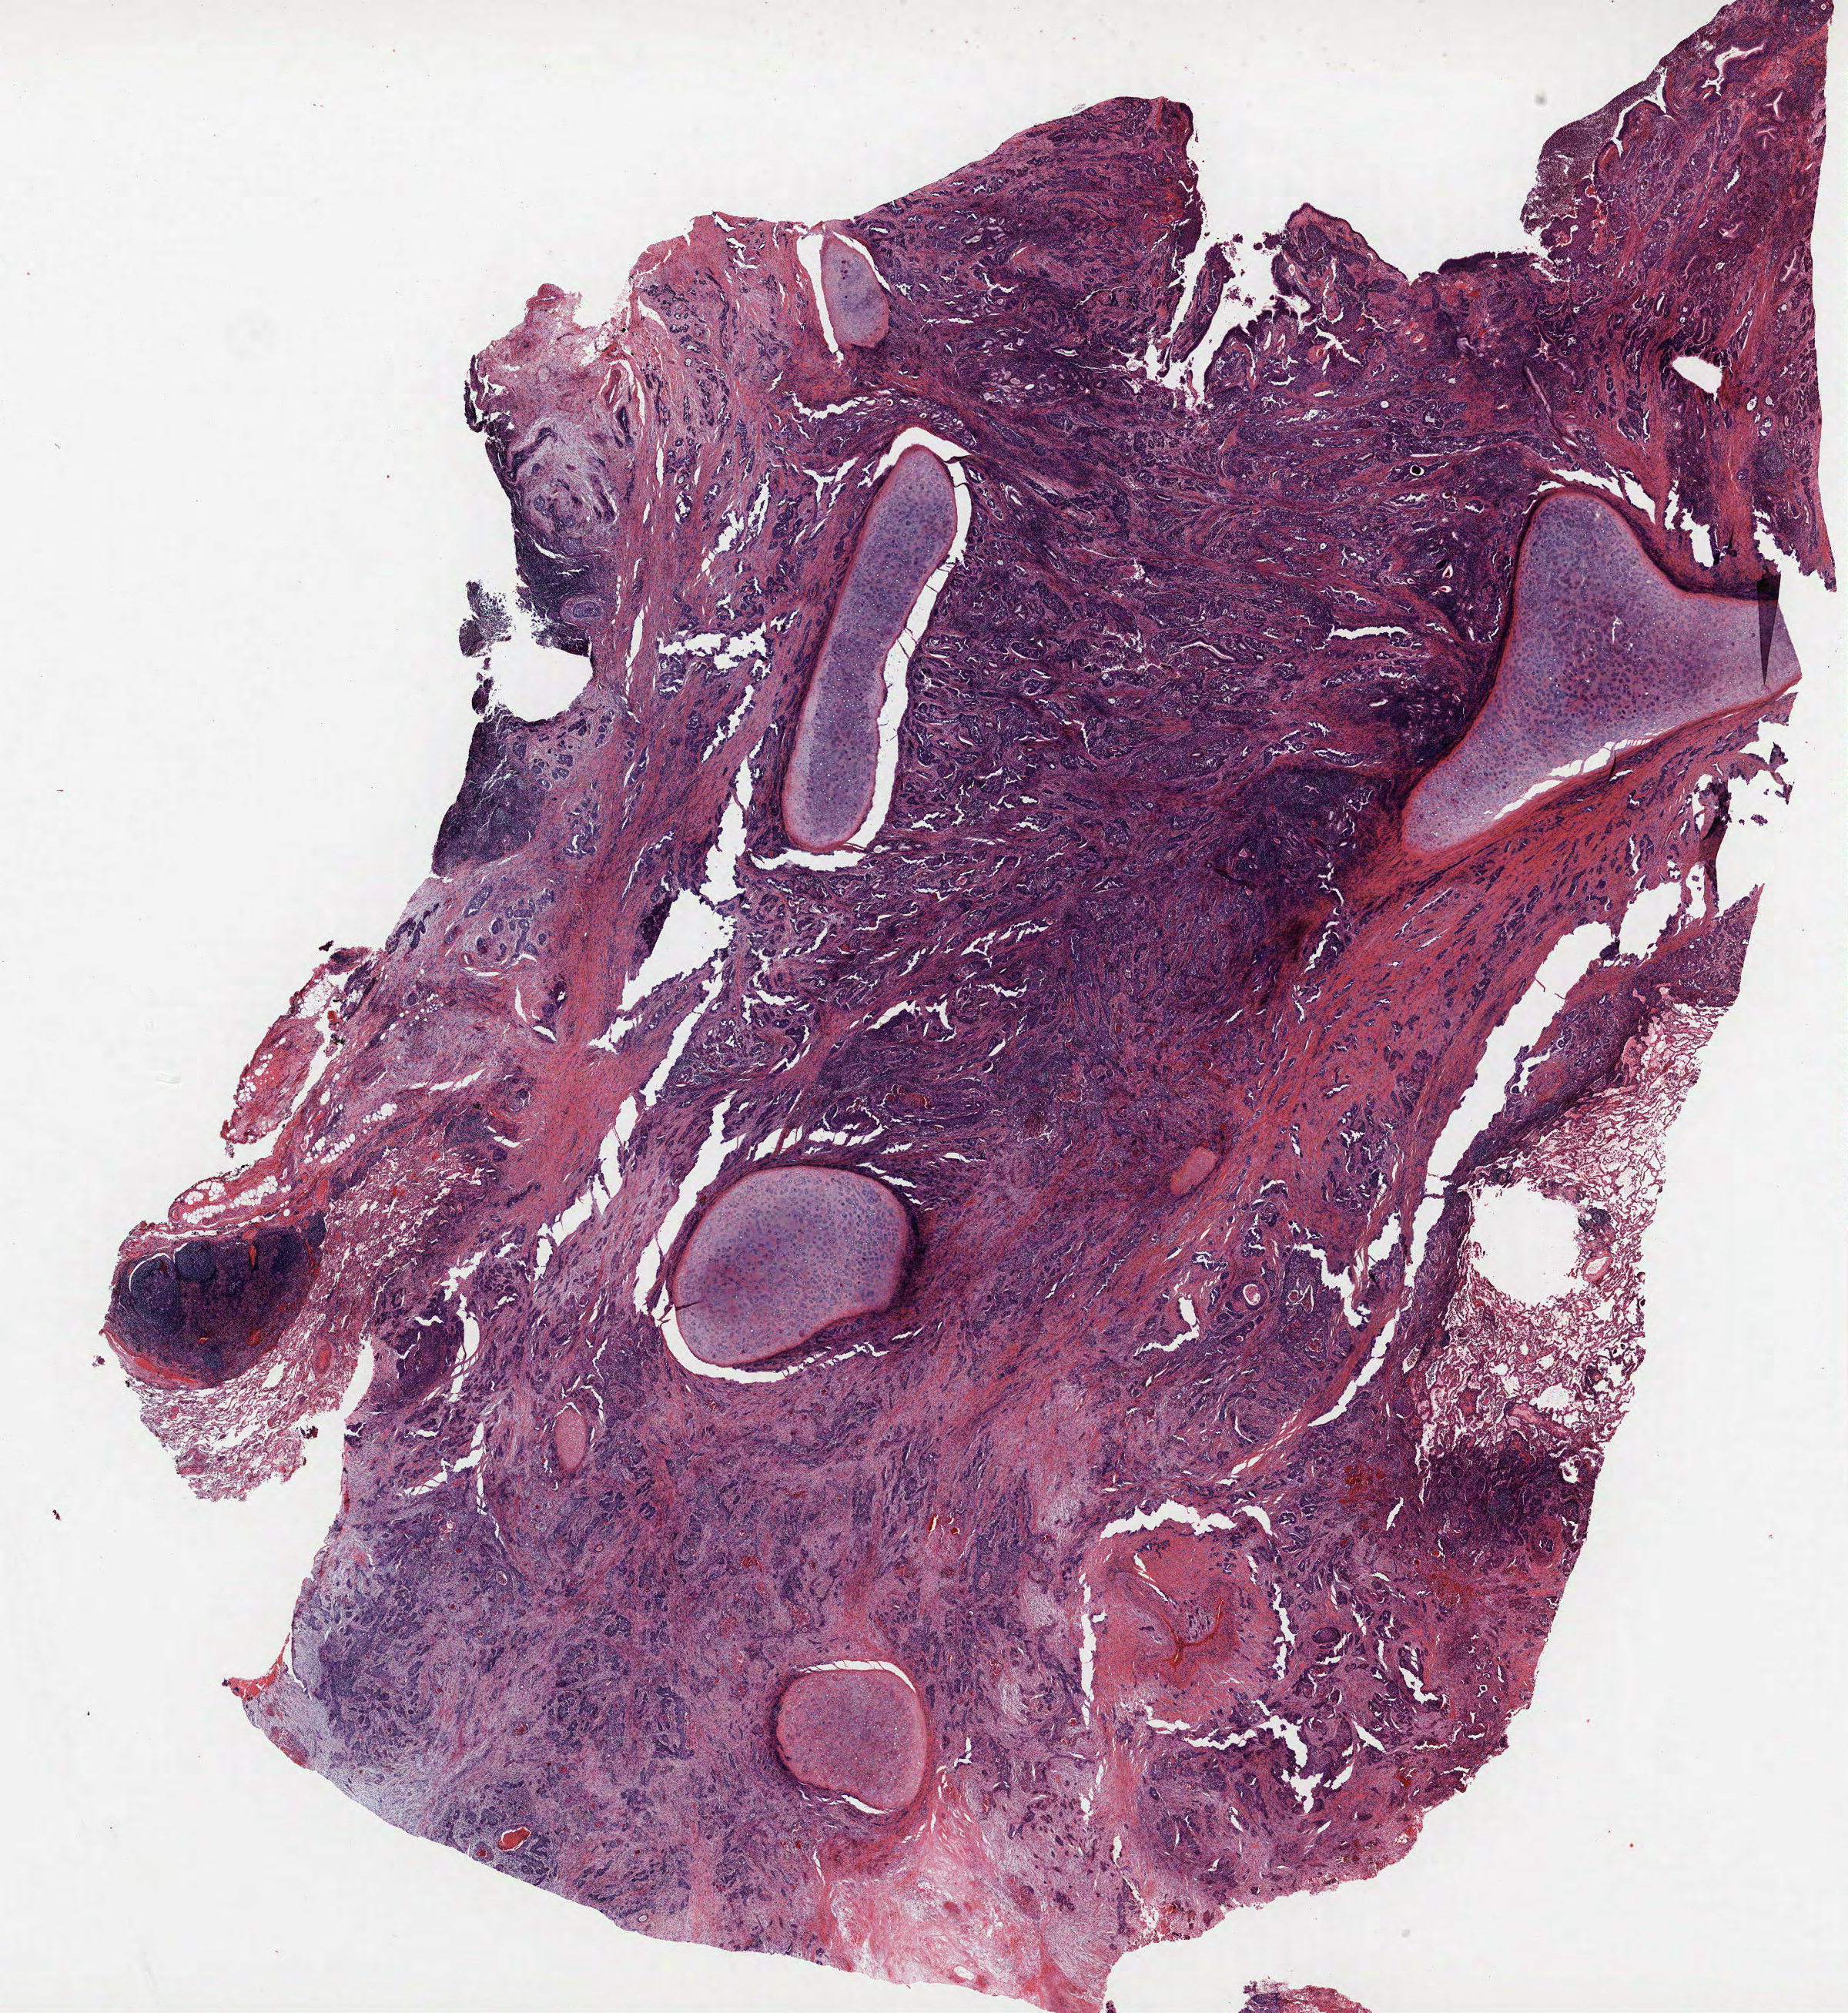
H&E whole-slide image, whole scanned area (about 19.2 x 20.9 mm, slide scanned at 40x) shown as a low-resolution overview; formalin-fixed paraffin-embedded (FFPE) section; lung tissue. Male, age 57 at enrolment. Former smoker at enrolment. Grade: poorly differentiated (G3).
Participant's lung-cancer diagnosis: Squamous cell carcinoma, NOS. Stage (AJCC 6th edition): IIA. Primary tumour location (clinical record): right upper lobe. Tumour size (pathology): 30 mm.